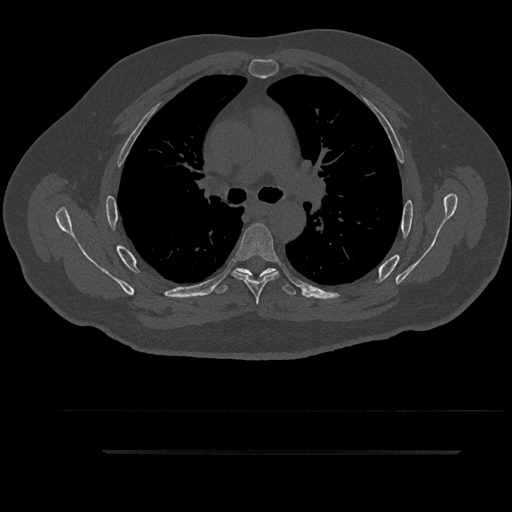
CT including the spine, one axial slice; slice 616 of 797 in the series (ordered by position); reconstruction kernel Br40s/3; bone window (W 1800 / L 400 HU); 0.5 mm slice thickness; 512 × 512 image matrix. Male patient, age 63 years. Case-level facts recorded for this patient, not image findings: primary cancer: renal; vertebrae with lytic lesions (as recorded): T8.
Annotated regions visible in this slice (semi-automatically segmented with operator editing):
- T5 vertebra: bounding box (x1, y1, x2, y2) in pixels: (232, 224, 279, 304)
- T6 vertebra: (212, 268, 296, 295)